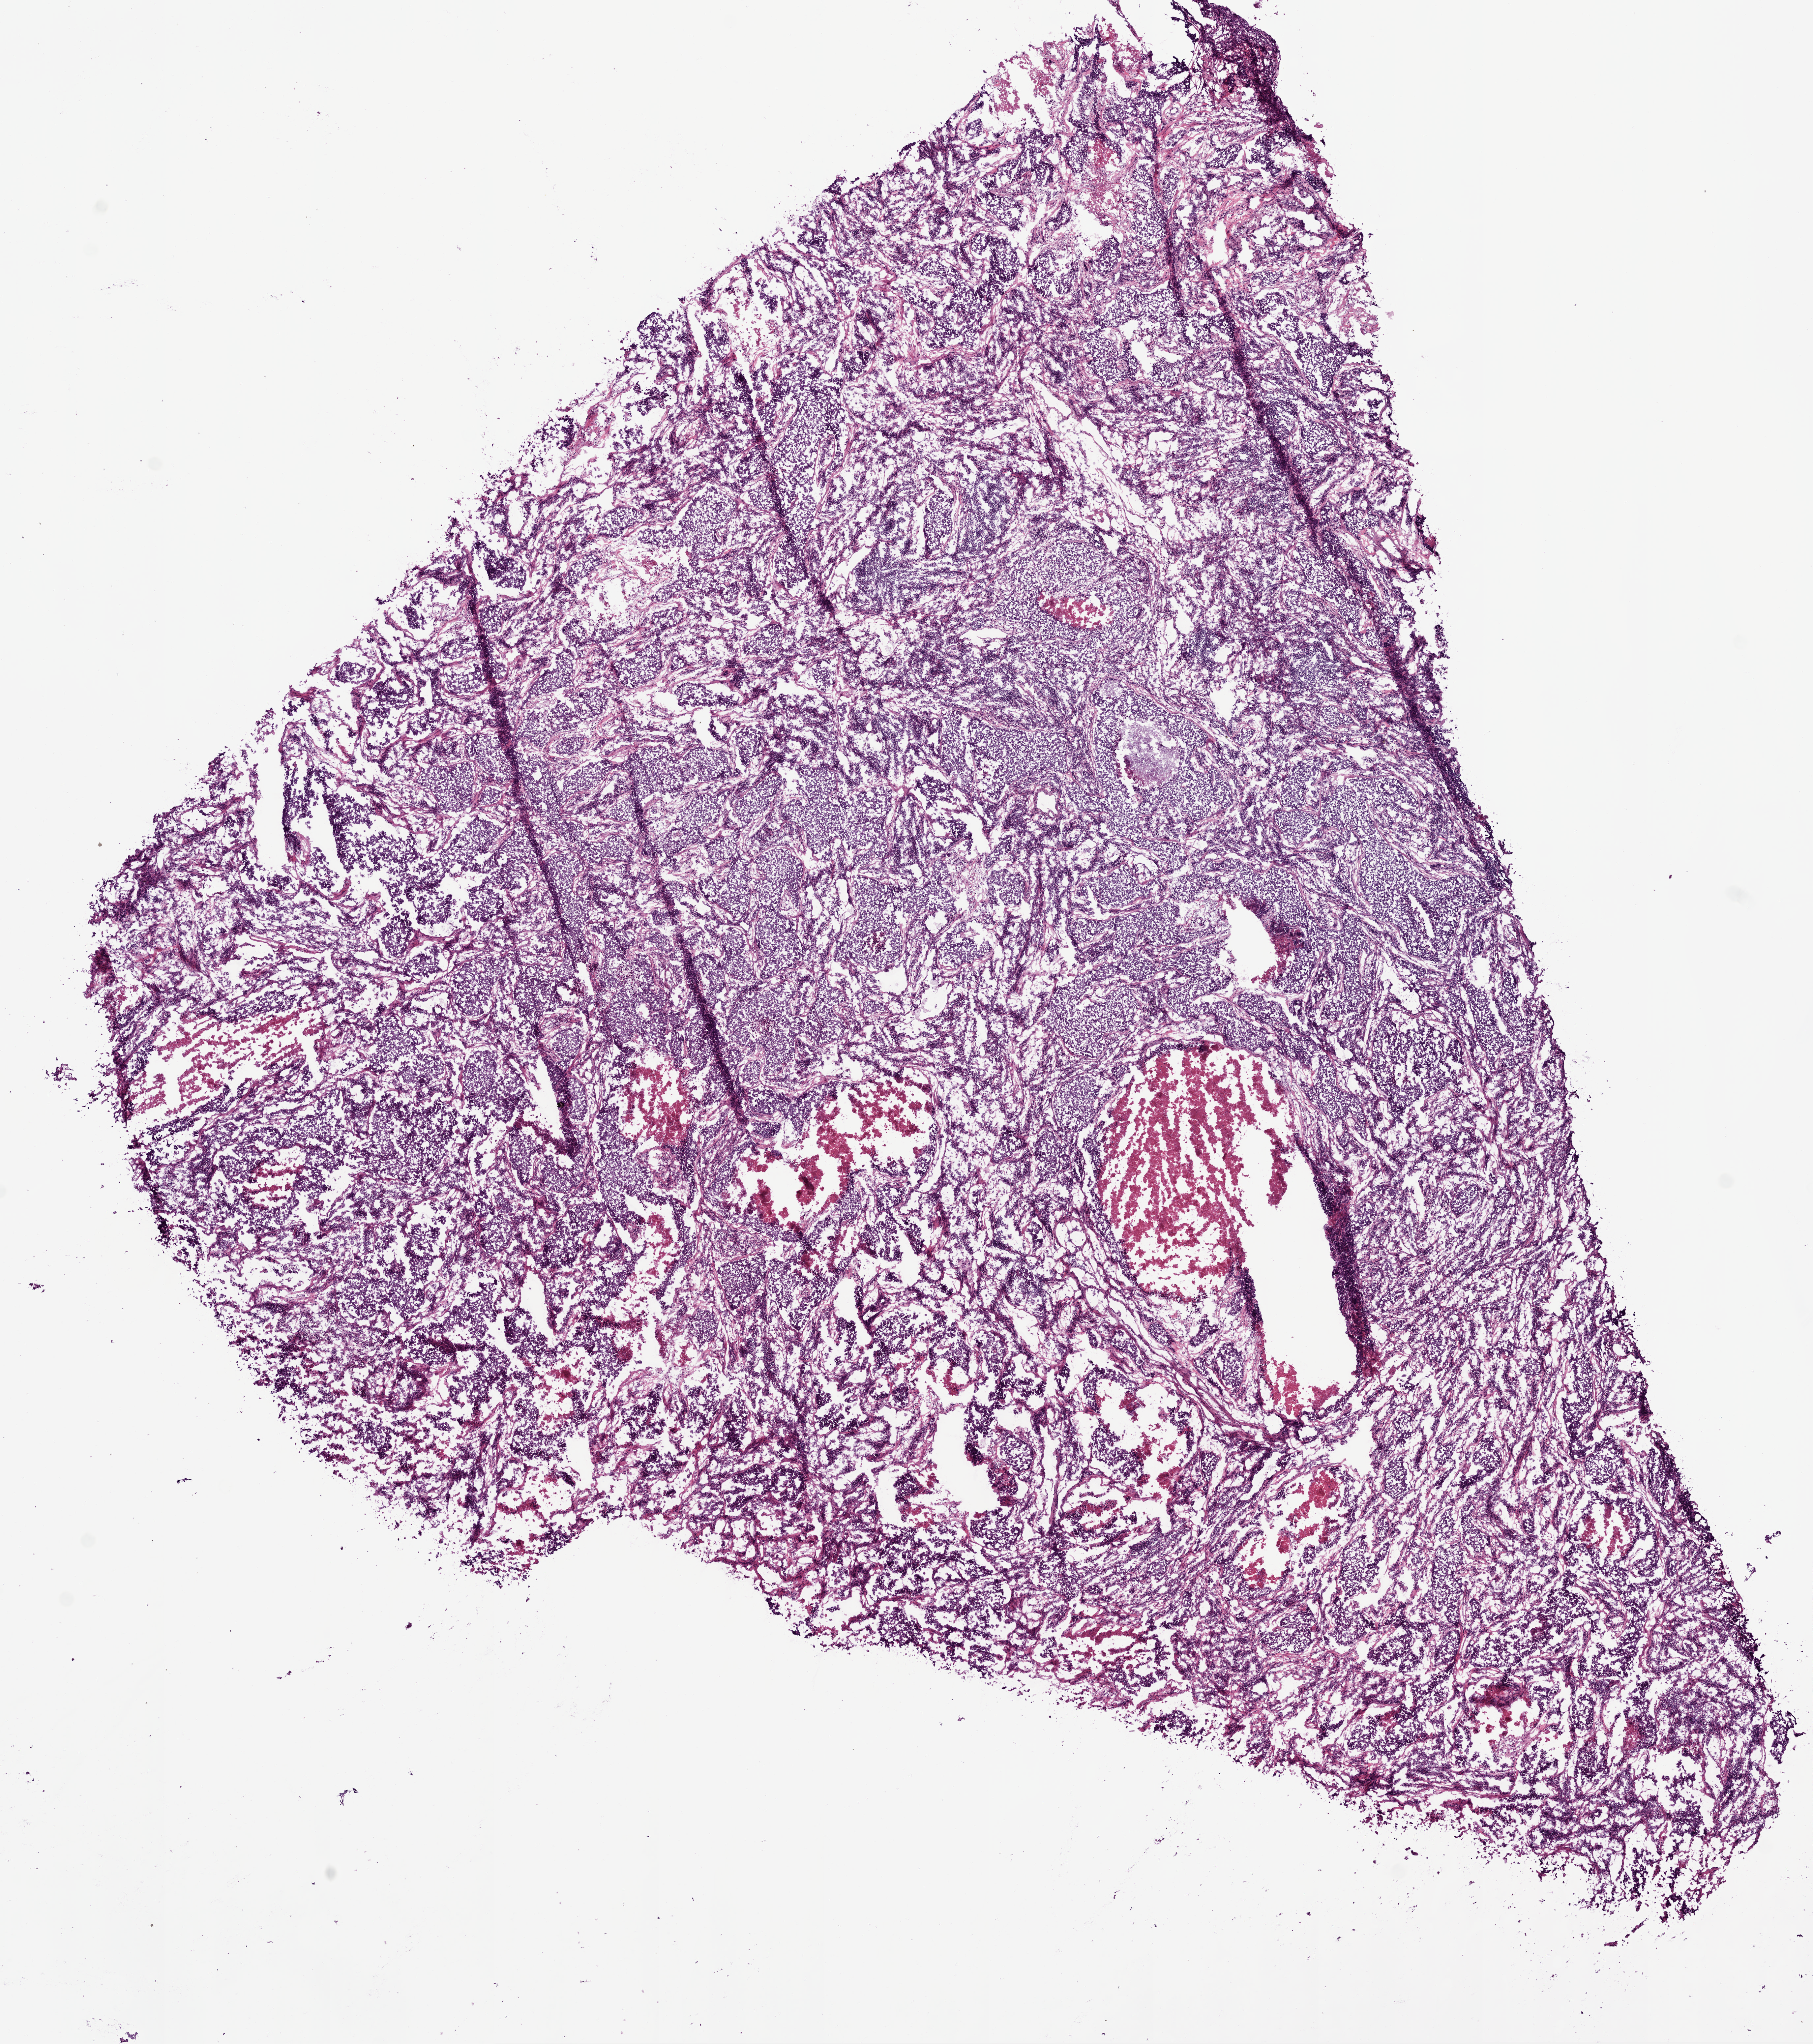
Whole-slide histology image, H&E-stained, shown as a low-resolution overview of the whole scanned area (about 11.0 x 12.4 mm), frozen section from the bottom of the tissue portion, primary tumour sample from the lung. Male patient; age at initial diagnosis 61 years. Composition of this section per pathologist review: tumour cells 80%, tumour nuclei 75%, normal cells 0%, stromal cells 12%, necrosis 8%. Inflammatory infiltration, as recorded: lymphocyte infiltration 12%, monocyte infiltration 0%, neutrophil infiltration 0%.
* pathologic diagnosis: Acinar cell carcinoma (lower lobe, lung)
* TNM: T2 N2 M0
* AJCC pathologic stage: IIIA (6th edition)